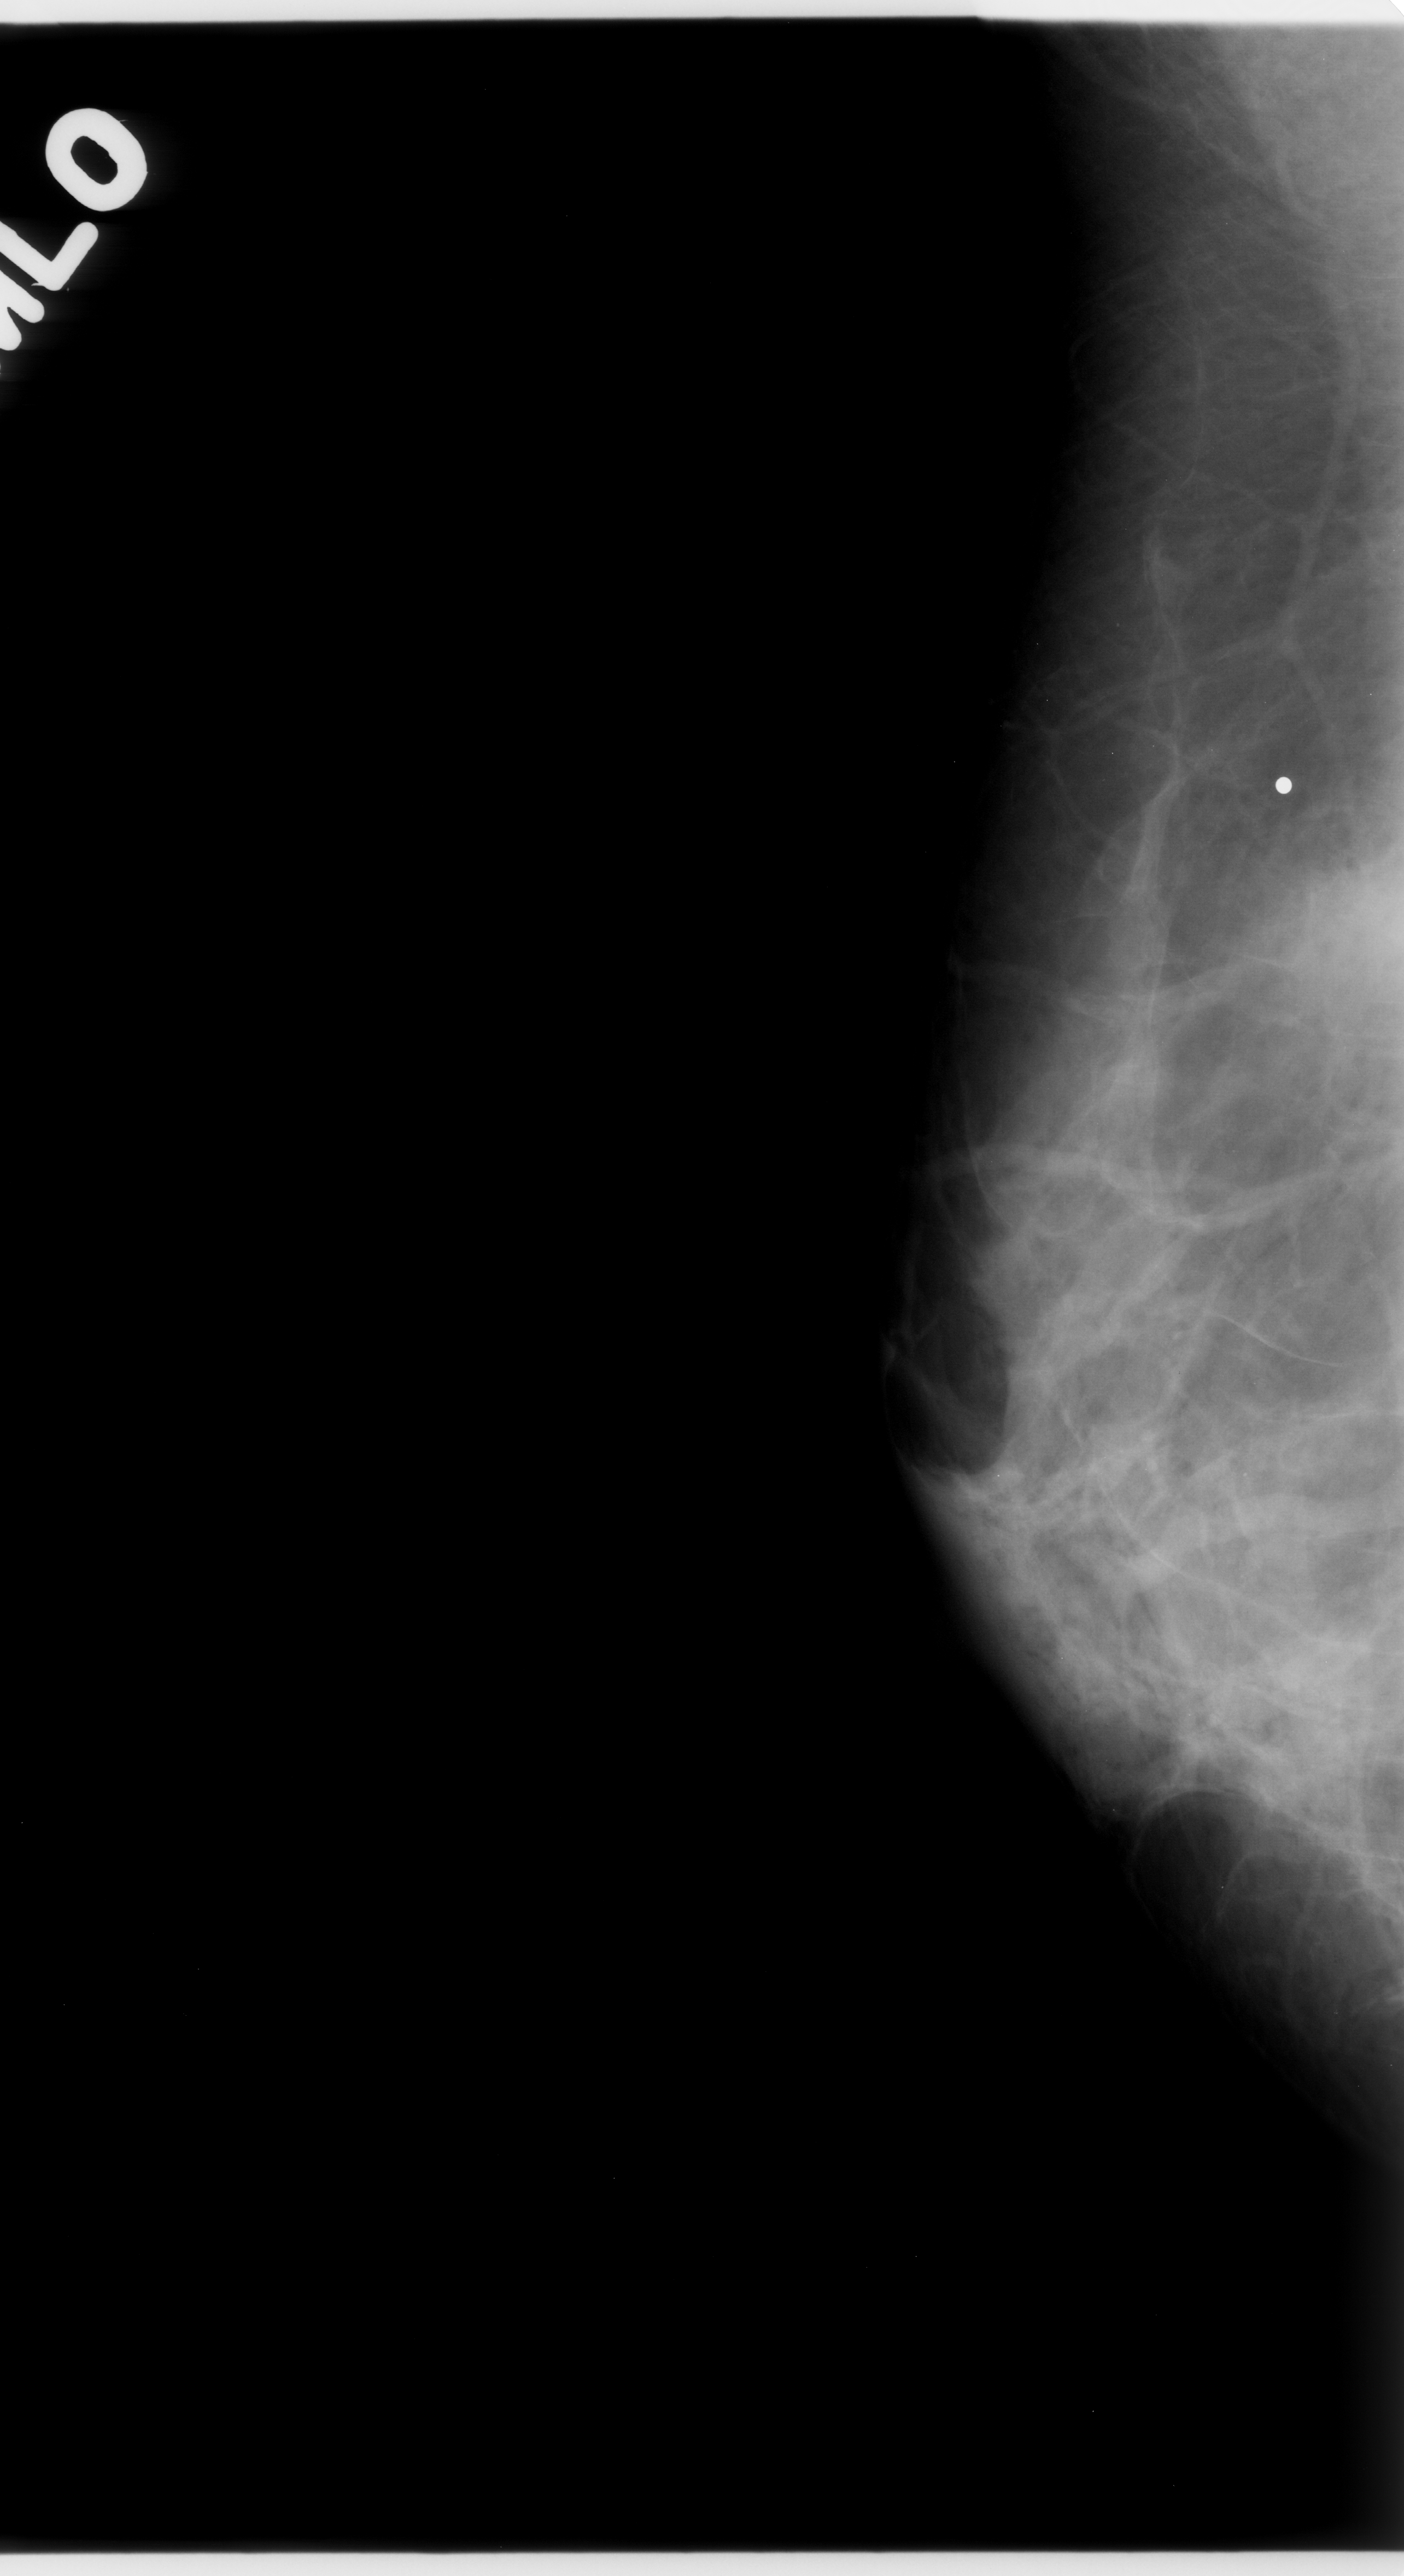
Digitized screen-film mammogram; right breast; mediolateral oblique (MLO) view; 1404 × 2576 image matrix.
Expert-marked regions of interest on this image (one box per marked abnormality):
- mass, shape oval, margins ill defined; BI-RADS assessment category 5; subtlety rating 4 on a 1 (subtle) to 5 (obvious) scale; pathology result (as recorded, not read from the image): malignant: bounding box <1206,757,1404,1105> (left, top, right, bottom; pixels)